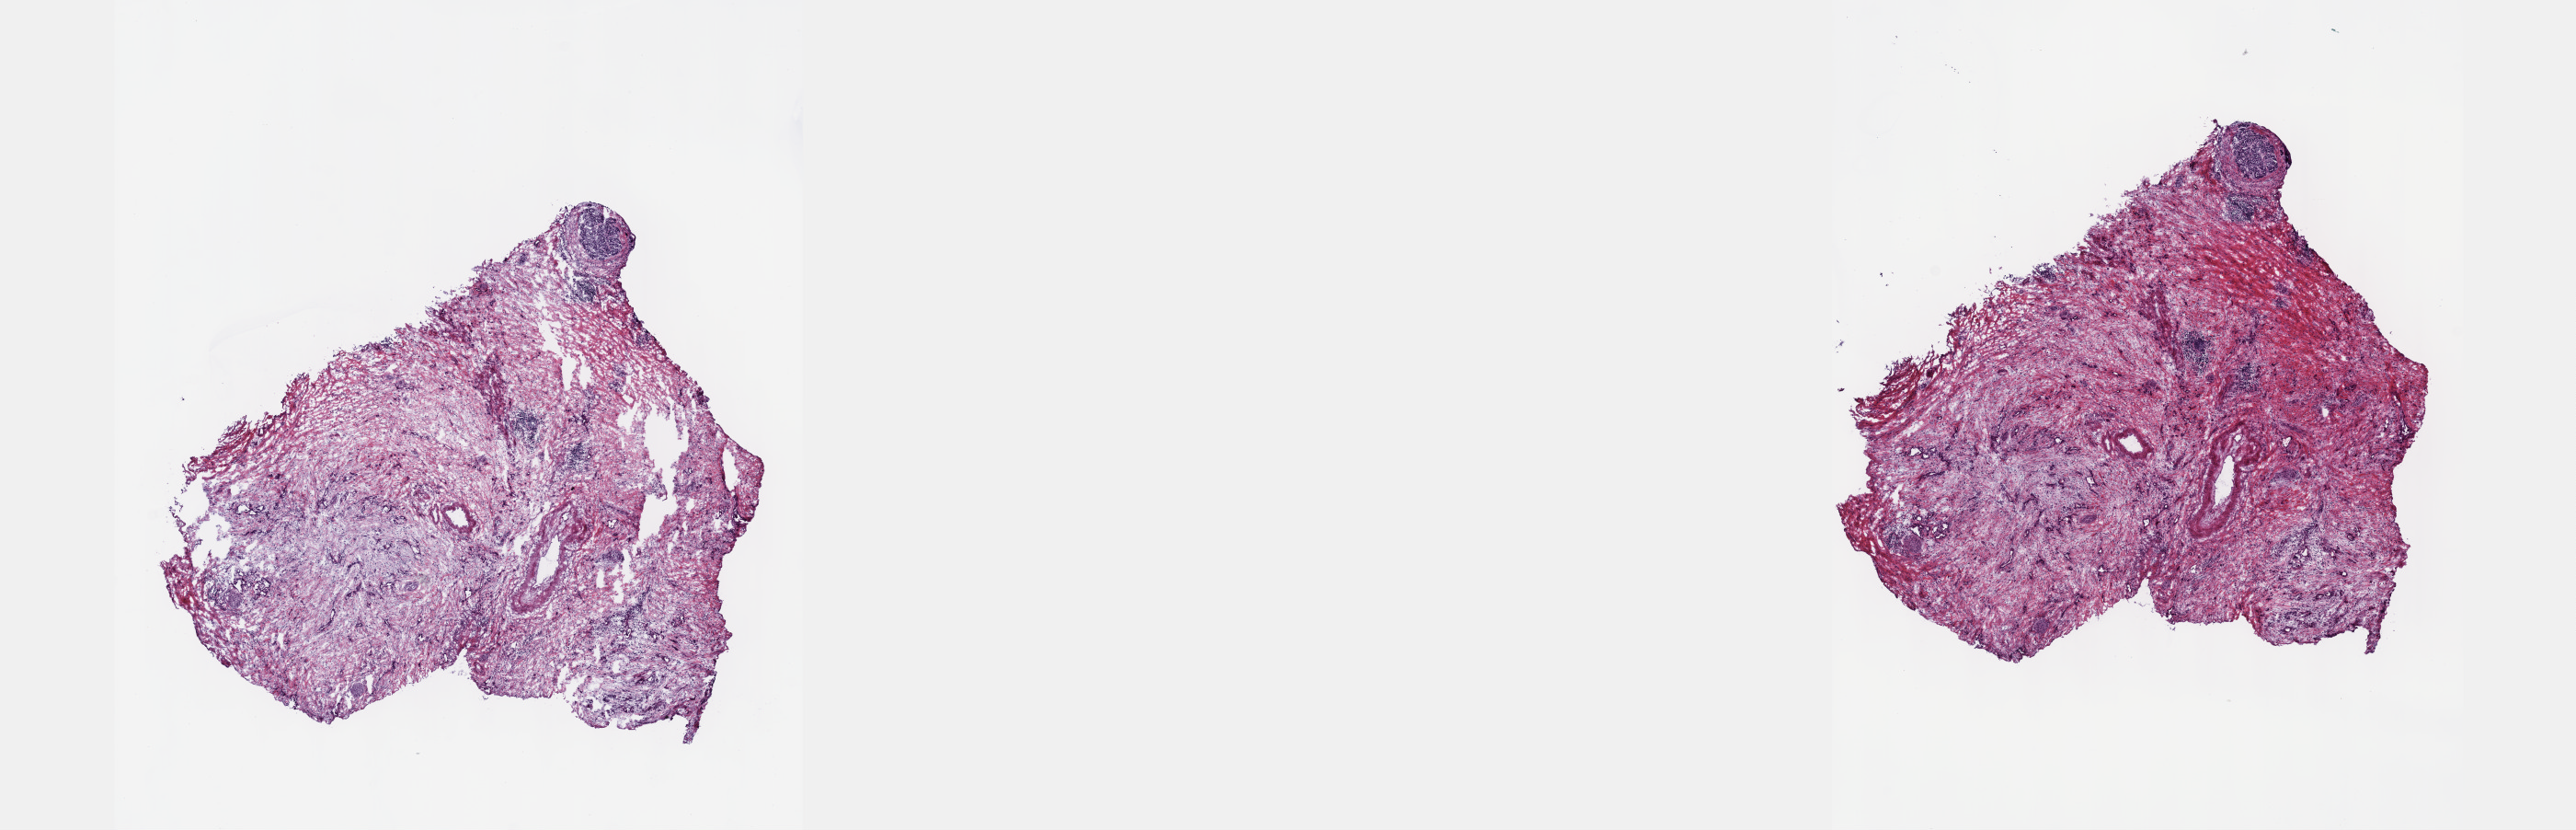
Hematoxylin and eosin (H&E) stained whole-slide image — whole scanned area (about 22.6 x 7.3 mm) shown as a low-resolution overview. Frozen section from the top of the tissue portion. Primary tumour sample from the pancreas. Patient: female, age at initial diagnosis 53 years. Histologic grade: G2 (moderately differentiated). Composition of this section per pathologist review: tumour cells 100%, tumour nuclei 5%, normal cells 0%, stromal cells 0%, necrosis 0%. Infiltration values recorded for this section: lymphocyte infiltration 5%, monocyte infiltration 0%, neutrophil infiltration 0%.
Pathologic diagnosis: Infiltrating duct carcinoma, NOS (head of pancreas). Lymph nodes positive (case pathology): 0 of 6 examined. AJCC pathologic stage: IB.